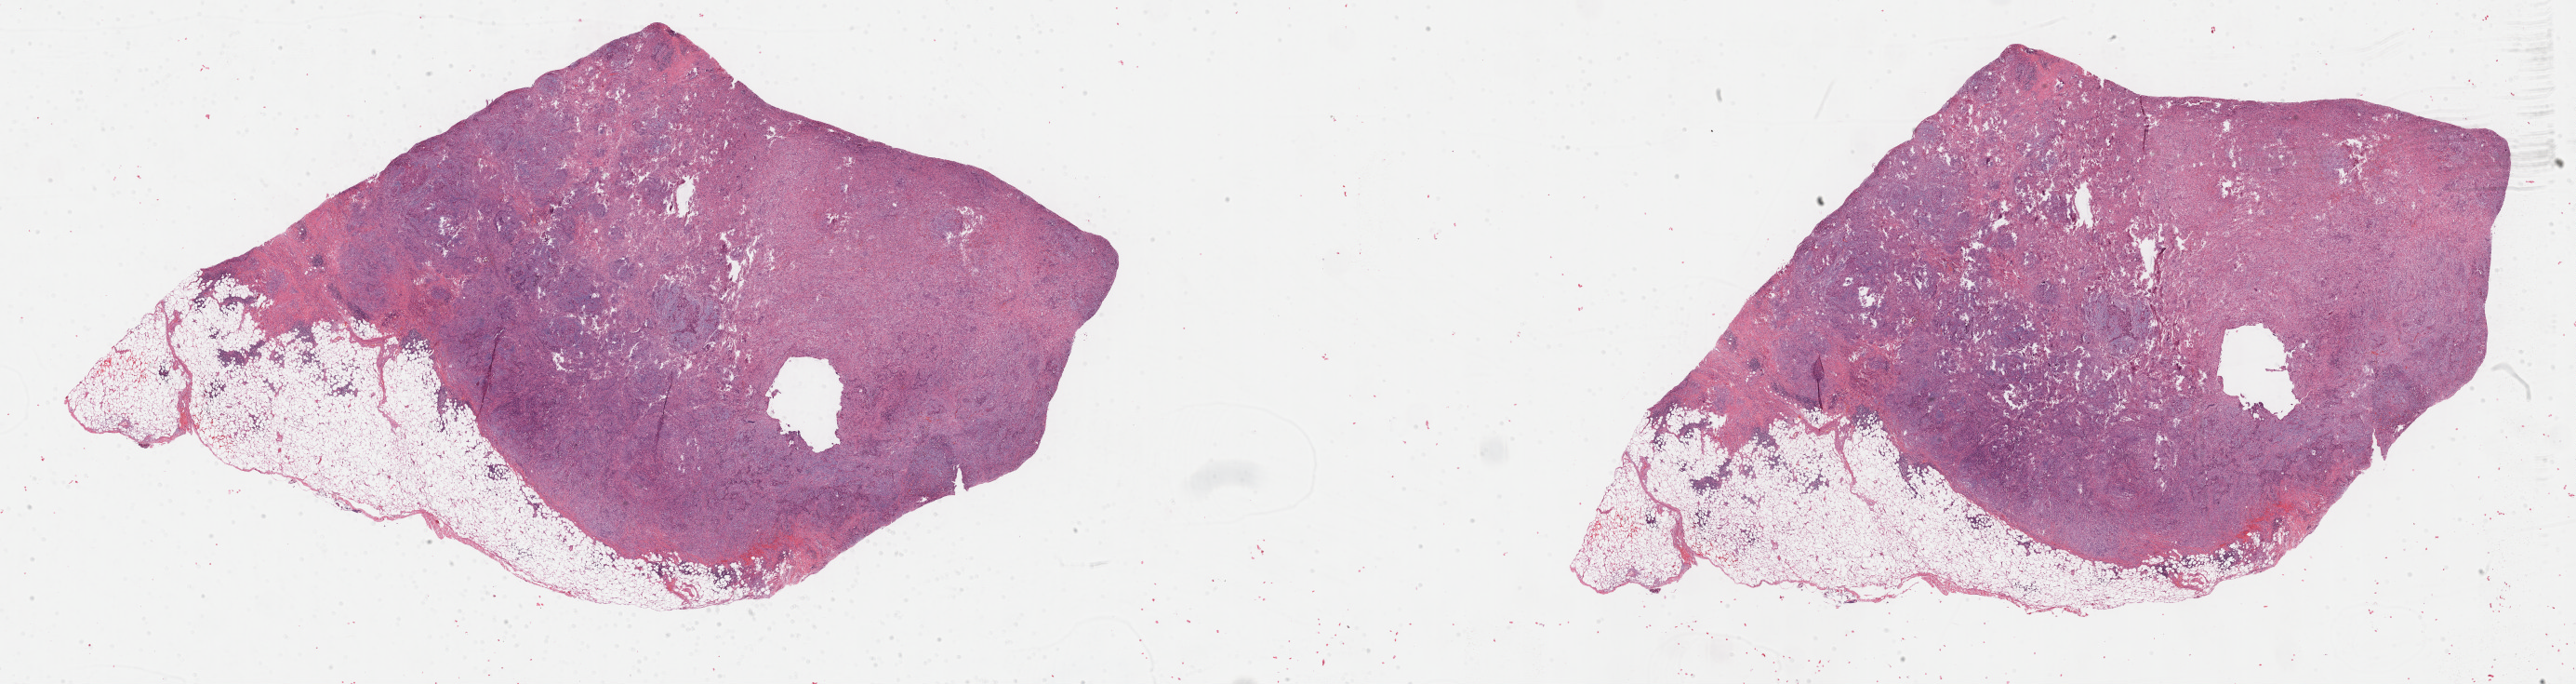
Whole-slide histology image, H&E-stained — whole scanned area (about 44.8 x 11.9 mm, acquisition: 40x scan) shown as a low-resolution overview; formalin-fixed paraffin-embedded (FFPE) diagnostic section; mesothelium, primary tumour sample. Male, age 57 years at initial diagnosis.
* pathologic diagnosis: Epithelioid mesothelioma, malignant (pleura, NOS)
* AJCC pathologic stage: III